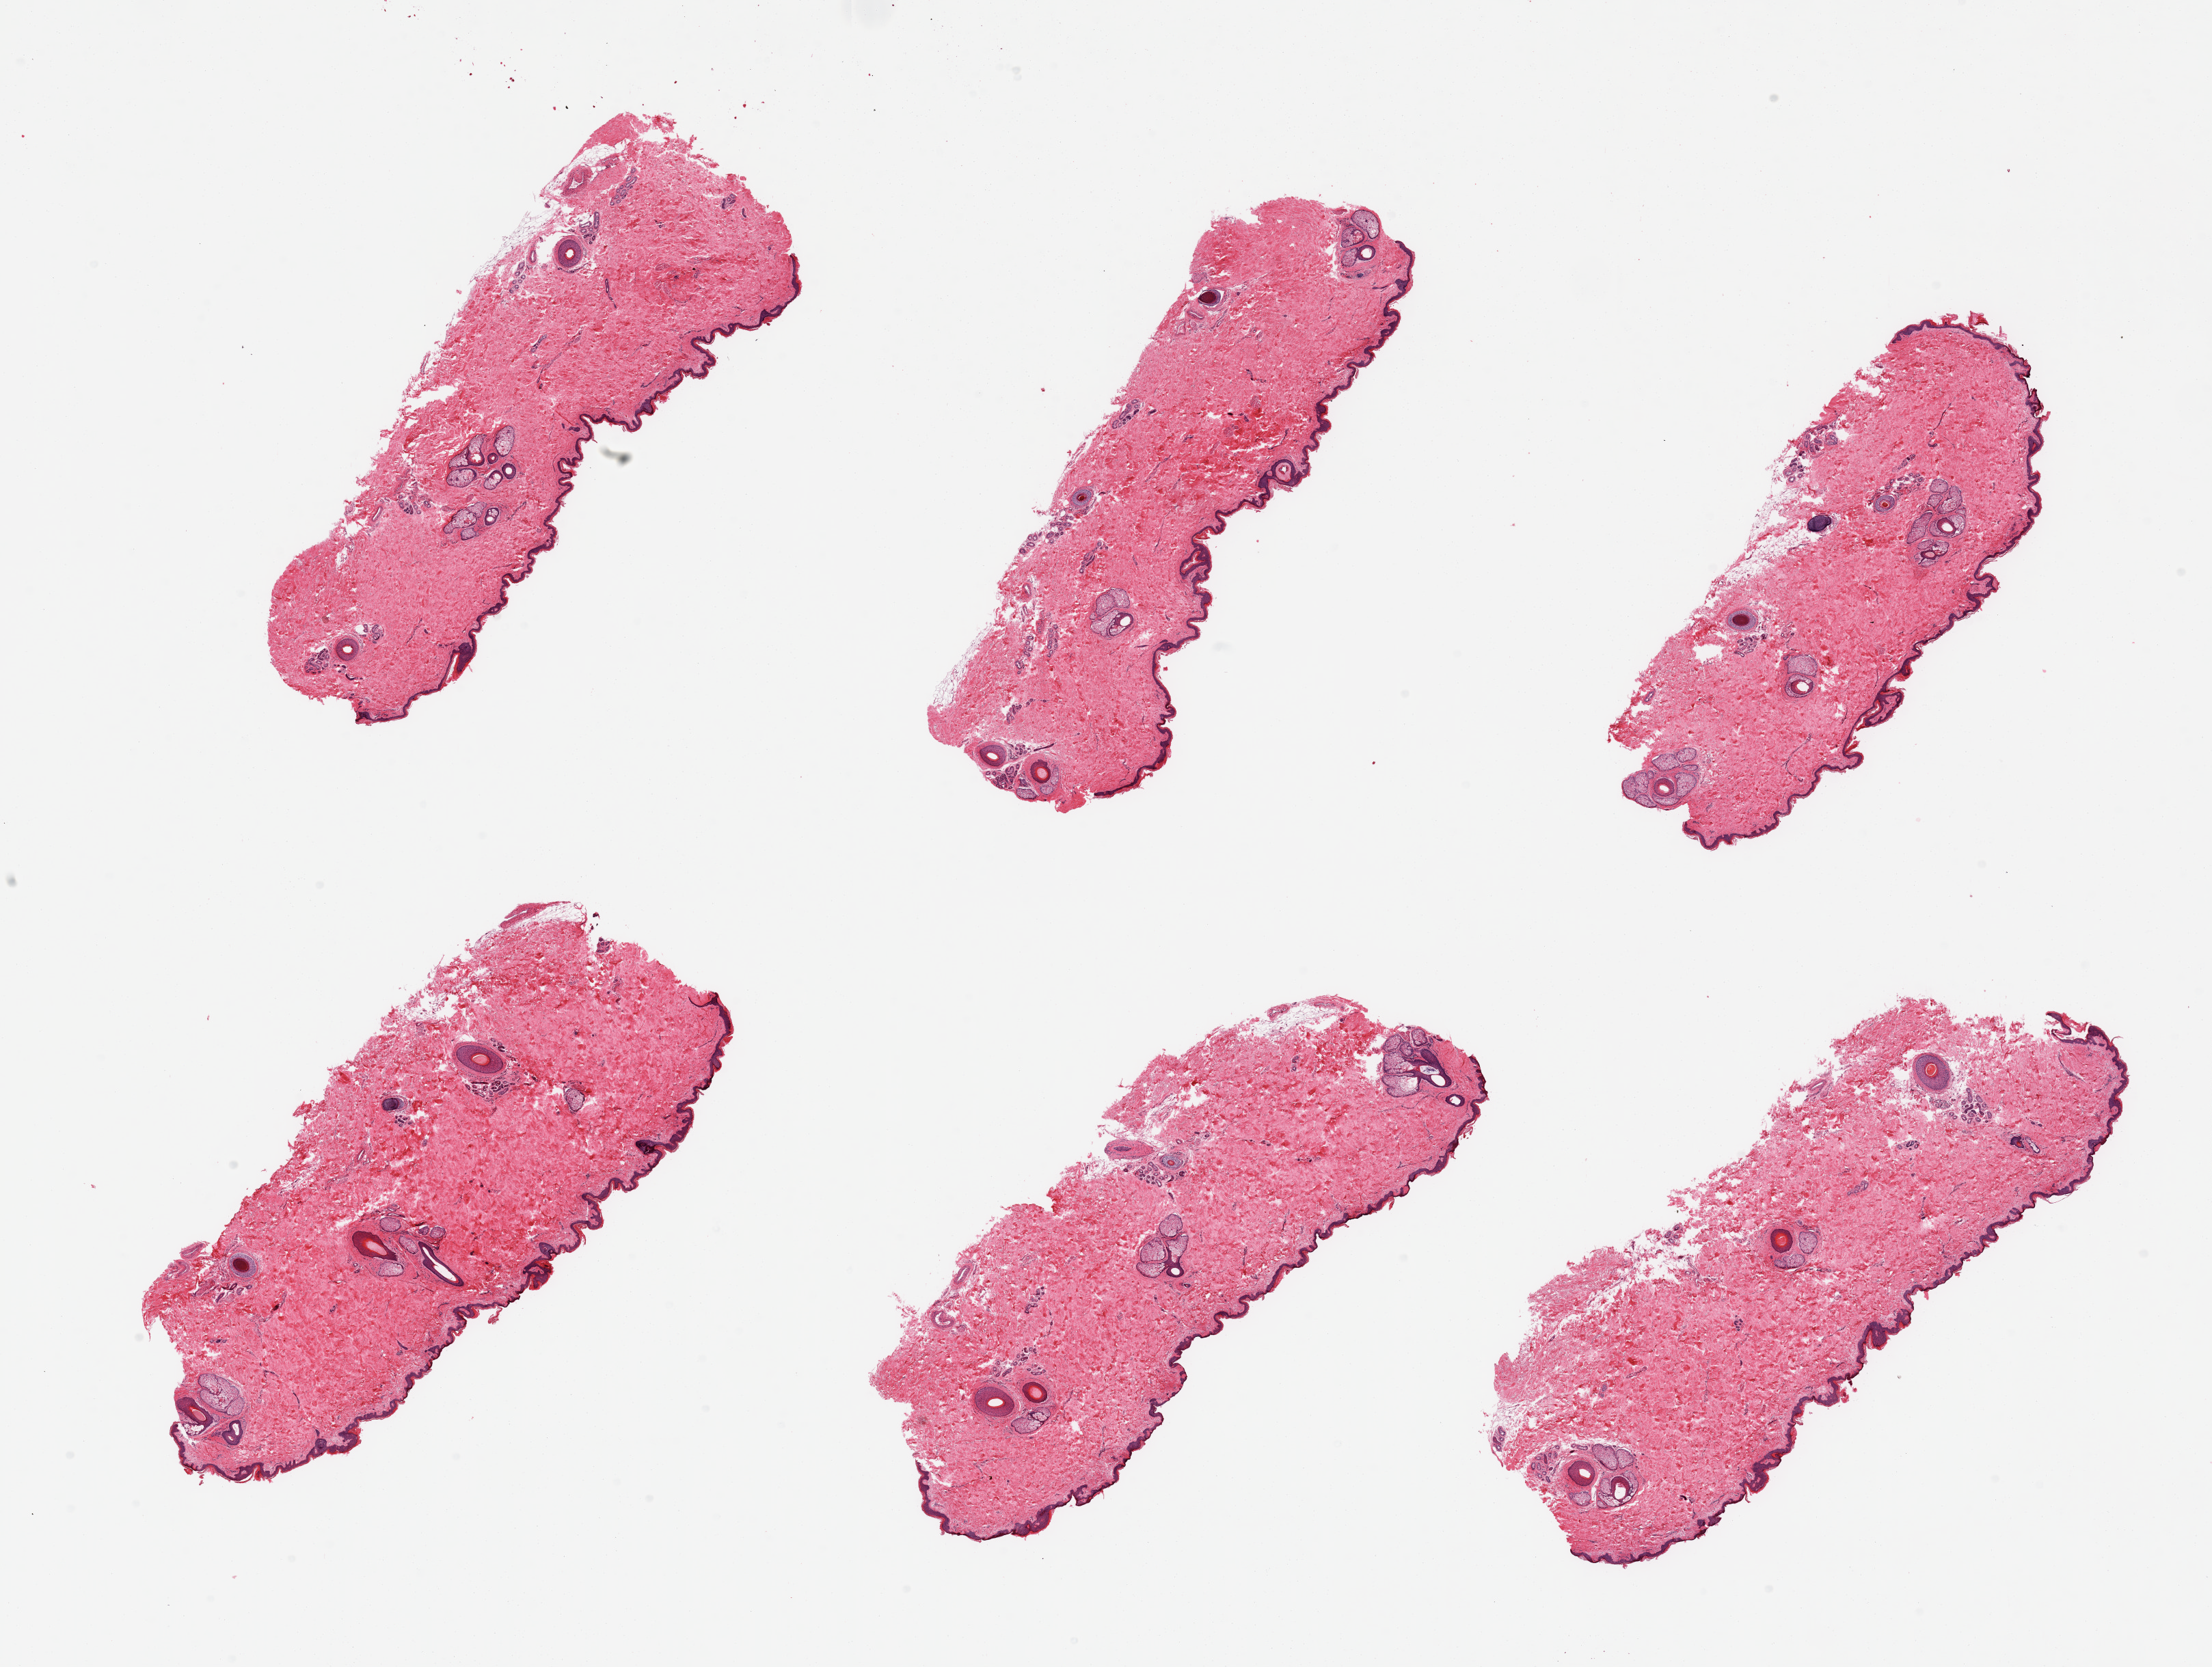
Digitized H&E-stained section, brightfield, whole scanned area (about 25.6 x 19.3 mm, from a 20x scan) shown as a low-resolution overview; PAXgene-fixed, paraffin-embedded tissue; section of skin of suprapubic region (target tissue); tissue donor sample. Donor: male.
Review note (as recorded): 6 pieces; well dissected; <5% dermal fat.